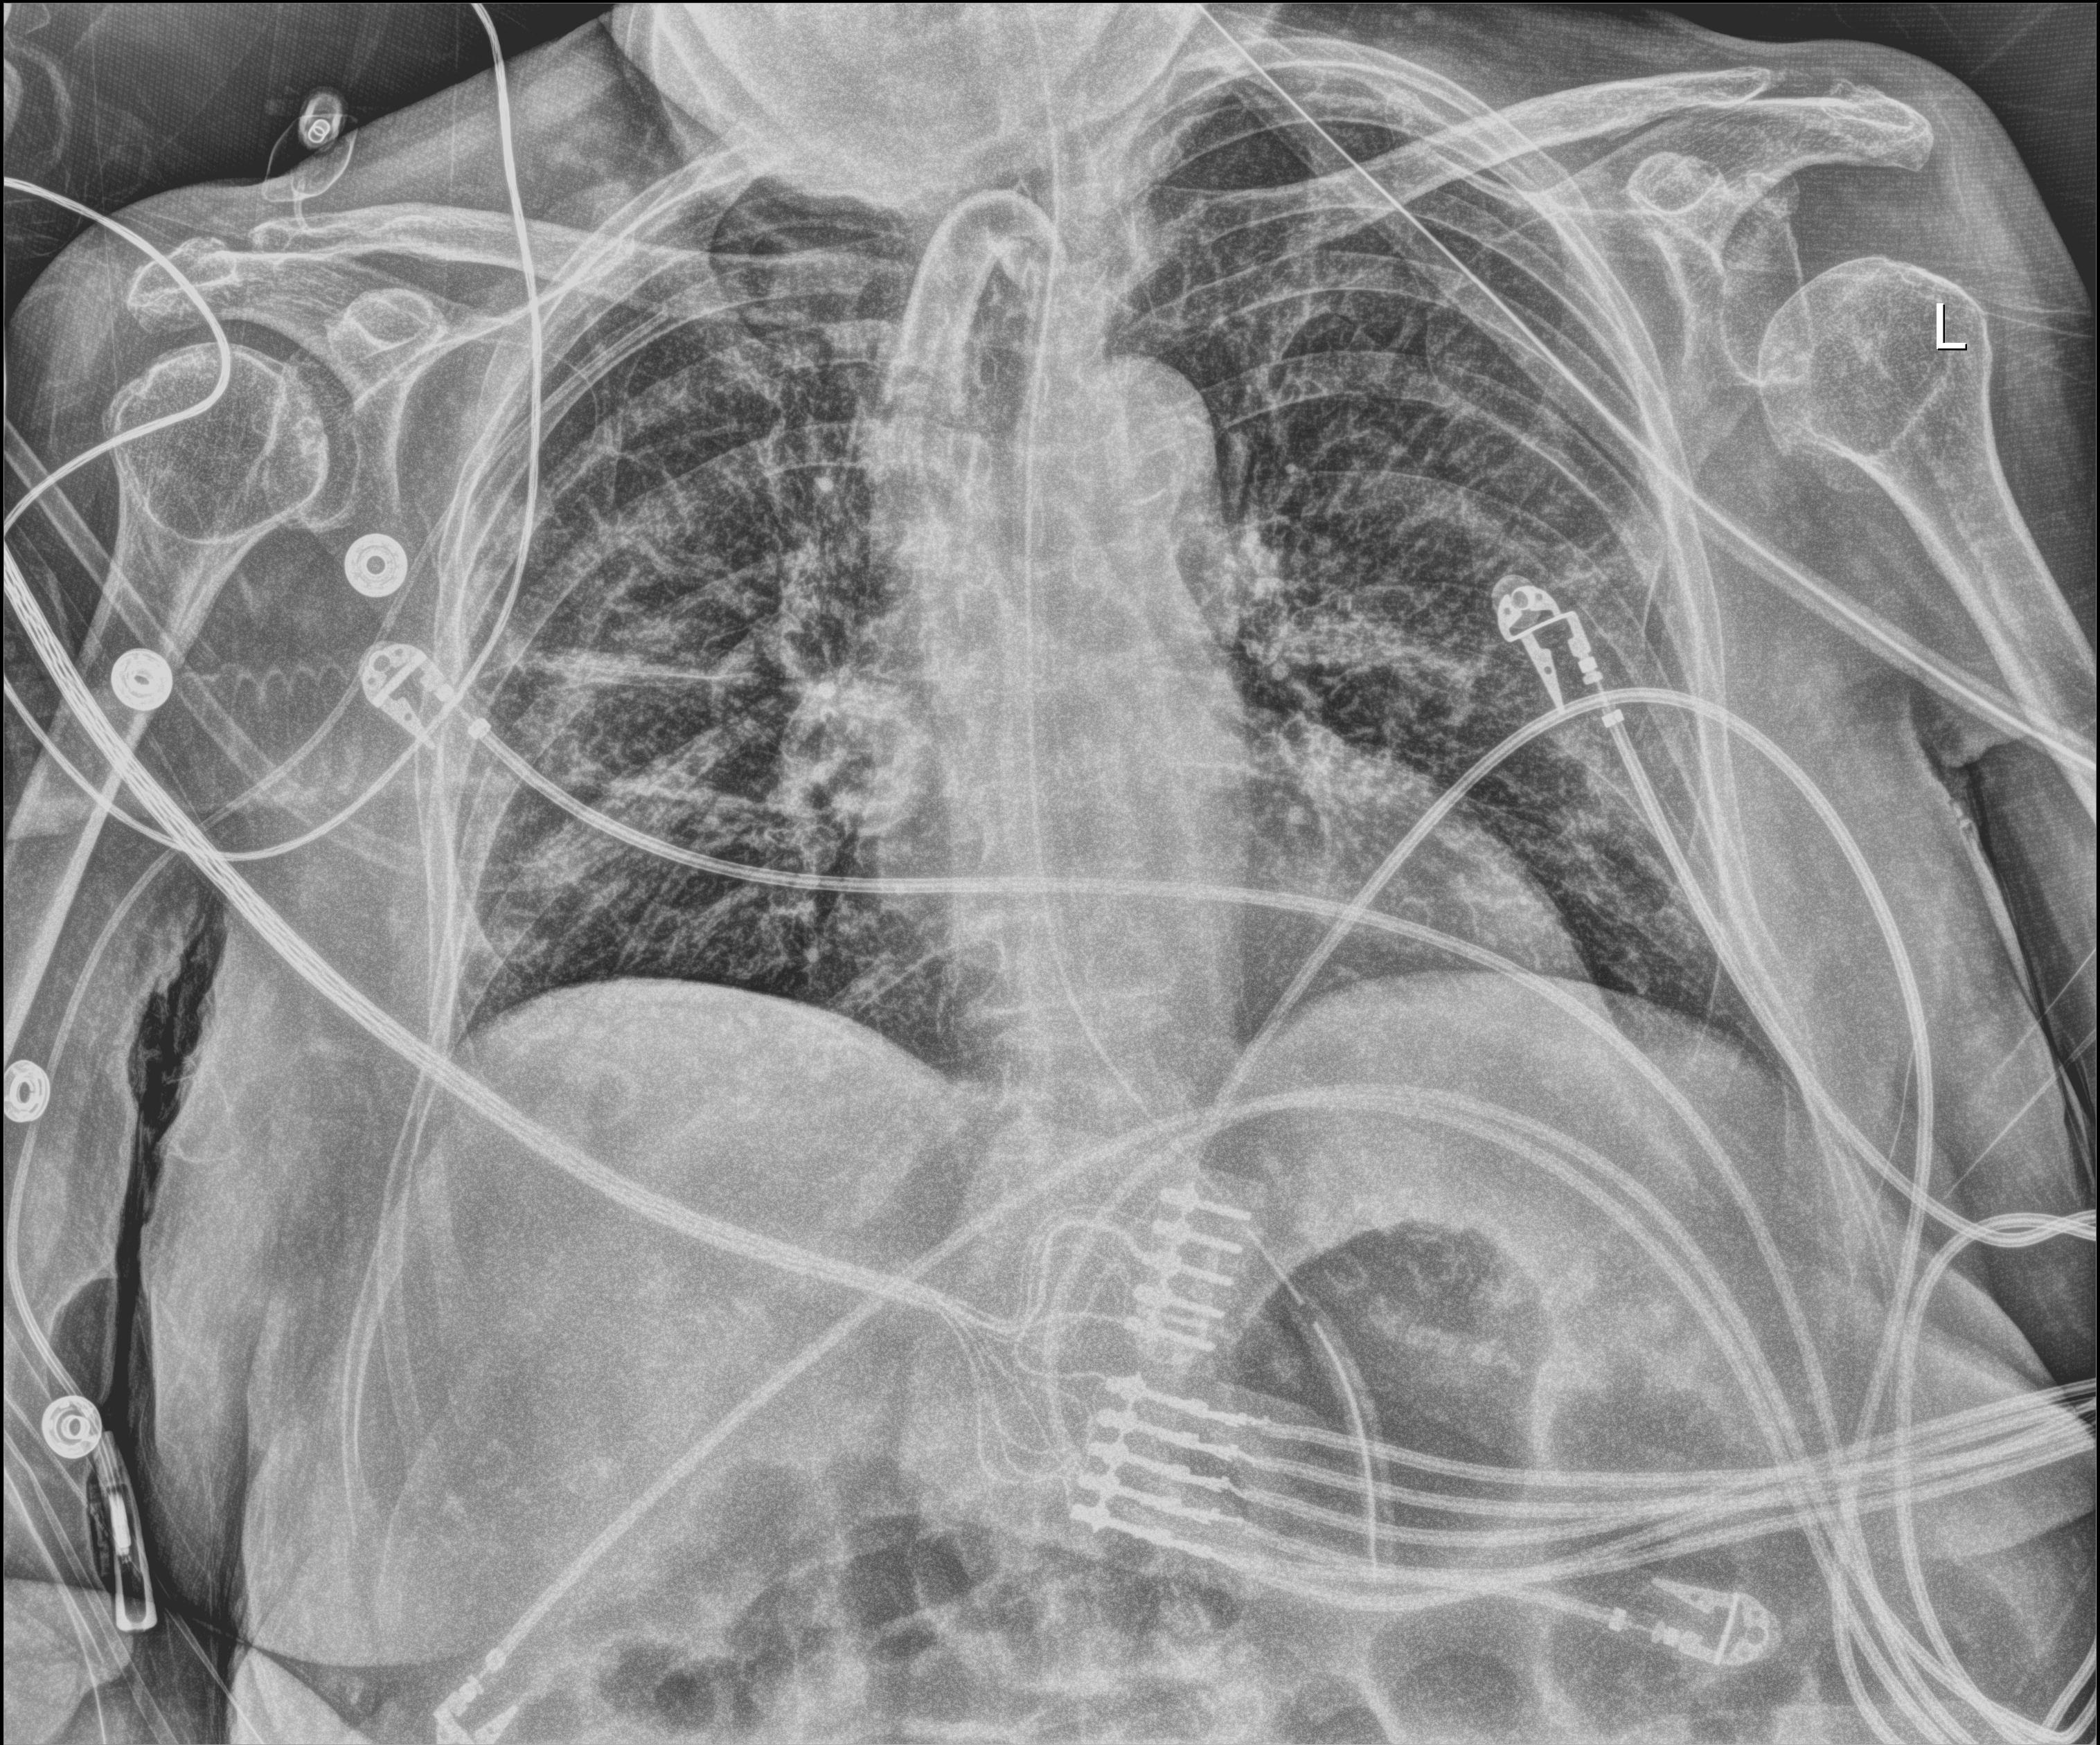
Chest X-ray; anteroposterior (AP) projection. Female patient hospitalised with COVID-19, age 75–90 years.
From the hospital-stay record, not from the radiograph (when in the stay this image was taken is not recorded):
- admitted to intensive care during this hospital stay: yes
- other chronic lung disease (admission record): yes
- mechanically ventilated during this hospital stay: yes